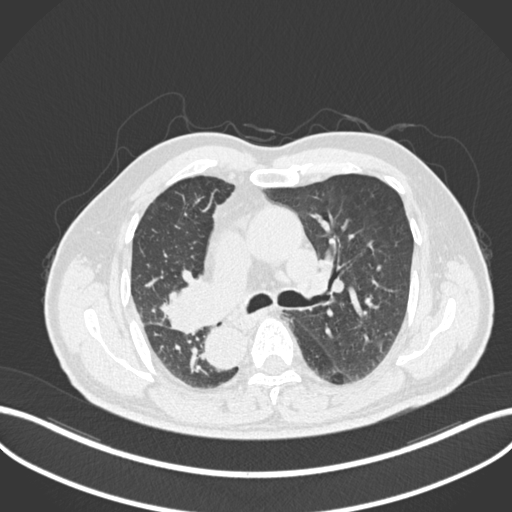
Chest CT, one axial slice. Position 143 of 206 along the scan axis. Reconstruction kernel B30f. 120 kVp. Lung window (W 1500 / L -600 HU). 1 mm slice thickness. 512 × 512 image matrix, field of view 400 × 400 mm. Male patient, age 67 years. From the clinical record (not read from this slice): clinical TNM (as recorded): T2a N0 M0.
Annotated regions visible in this slice (rectangle marked by the reading radiologist):
- lung tumour (recorded histology: squamous cell carcinoma): bounding box (x1, y1, x2, y2) in pixels: (157, 272, 214, 336)